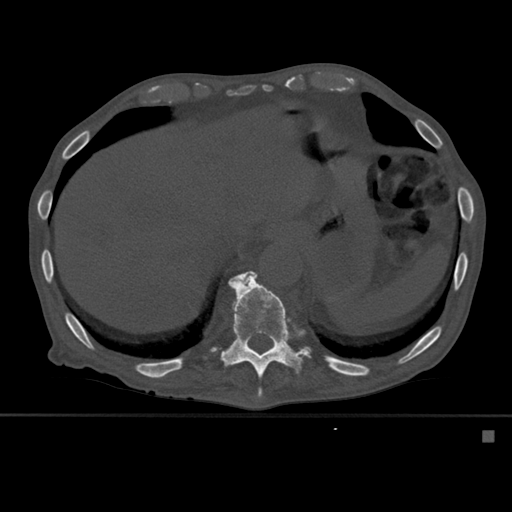
CT including the spine, one axial slice. Position 298 of 527 along the scan axis. Bone window (W 1800 / L 400 HU). 1.5 mm slice thickness. 512 × 512 image matrix. Patient: male, 78 years. From the clinical record (not read from this slice): primary cancer: prostate.
Outlined on this slice (semi-automatic segmentation, software-assisted and operator-edited):
- T10 vertebra: bounding box <239,274,263,399> (left, top, right, bottom; pixels)
- T11 vertebra: <213,271,310,380>